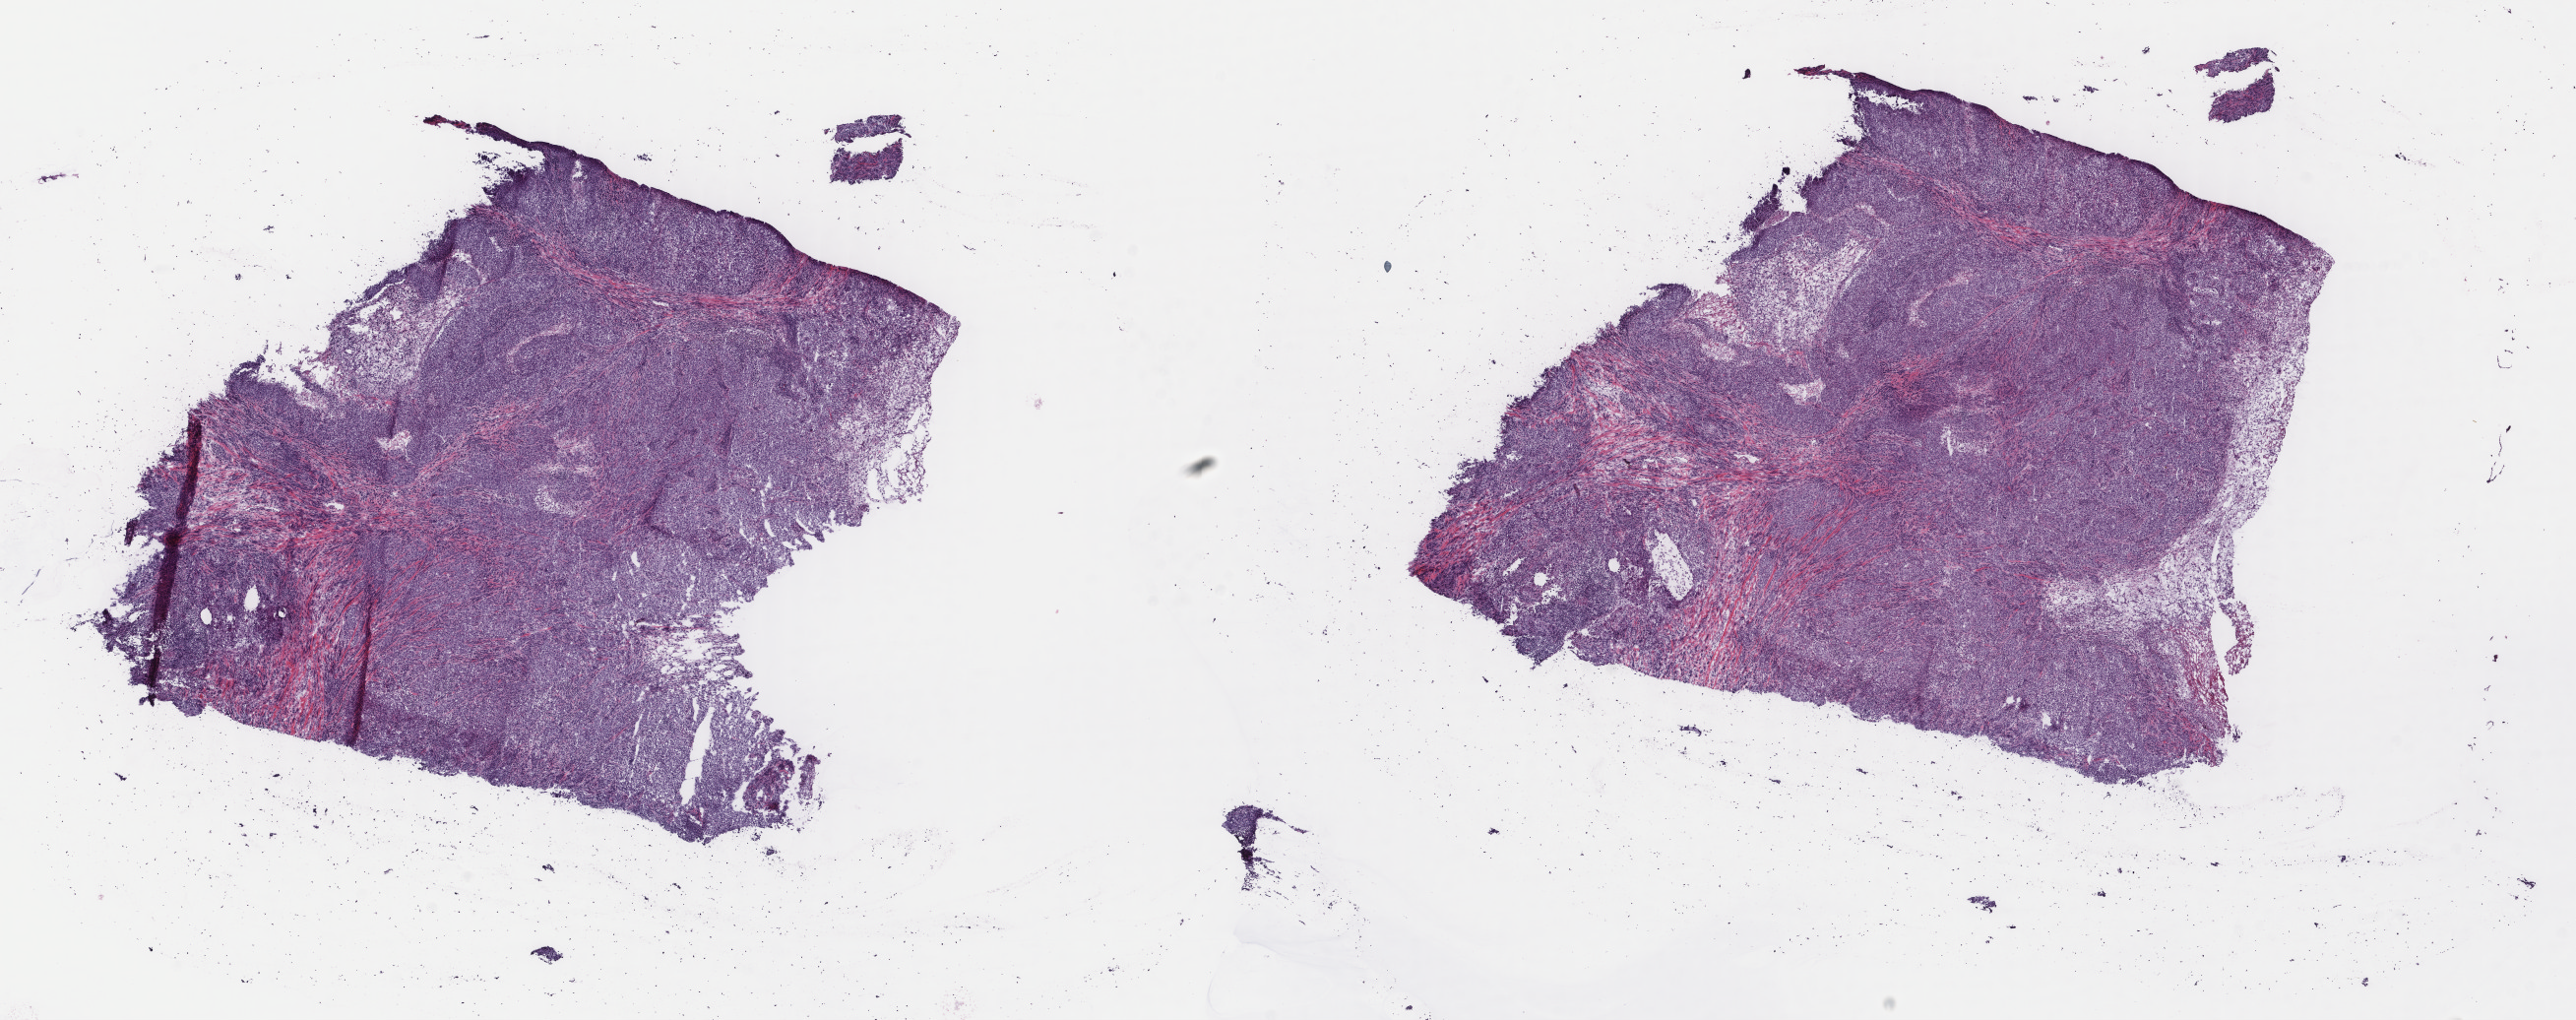
Hematoxylin and eosin (H&E) stained whole-slide image, low-resolution overview of the scanned area, about 20.8 x 8.2 mm (acquisition: 40x scan); frozen section from the top of the tissue portion; sample: primary tumour, breast. Female patient; age at initial diagnosis 49 years. Composition of this section per pathologist review: tumour cells 100%, tumour nuclei 93%, normal cells 0%, stromal cells 0%, necrosis 0%. Infiltration values recorded for this section: lymphocyte infiltration 0%, monocyte infiltration 0%, neutrophil infiltration 0%.
- diagnosis: Infiltrating duct carcinoma, NOS
- AJCC pathologic stage: IIA
- TNM: T2 N0 M0